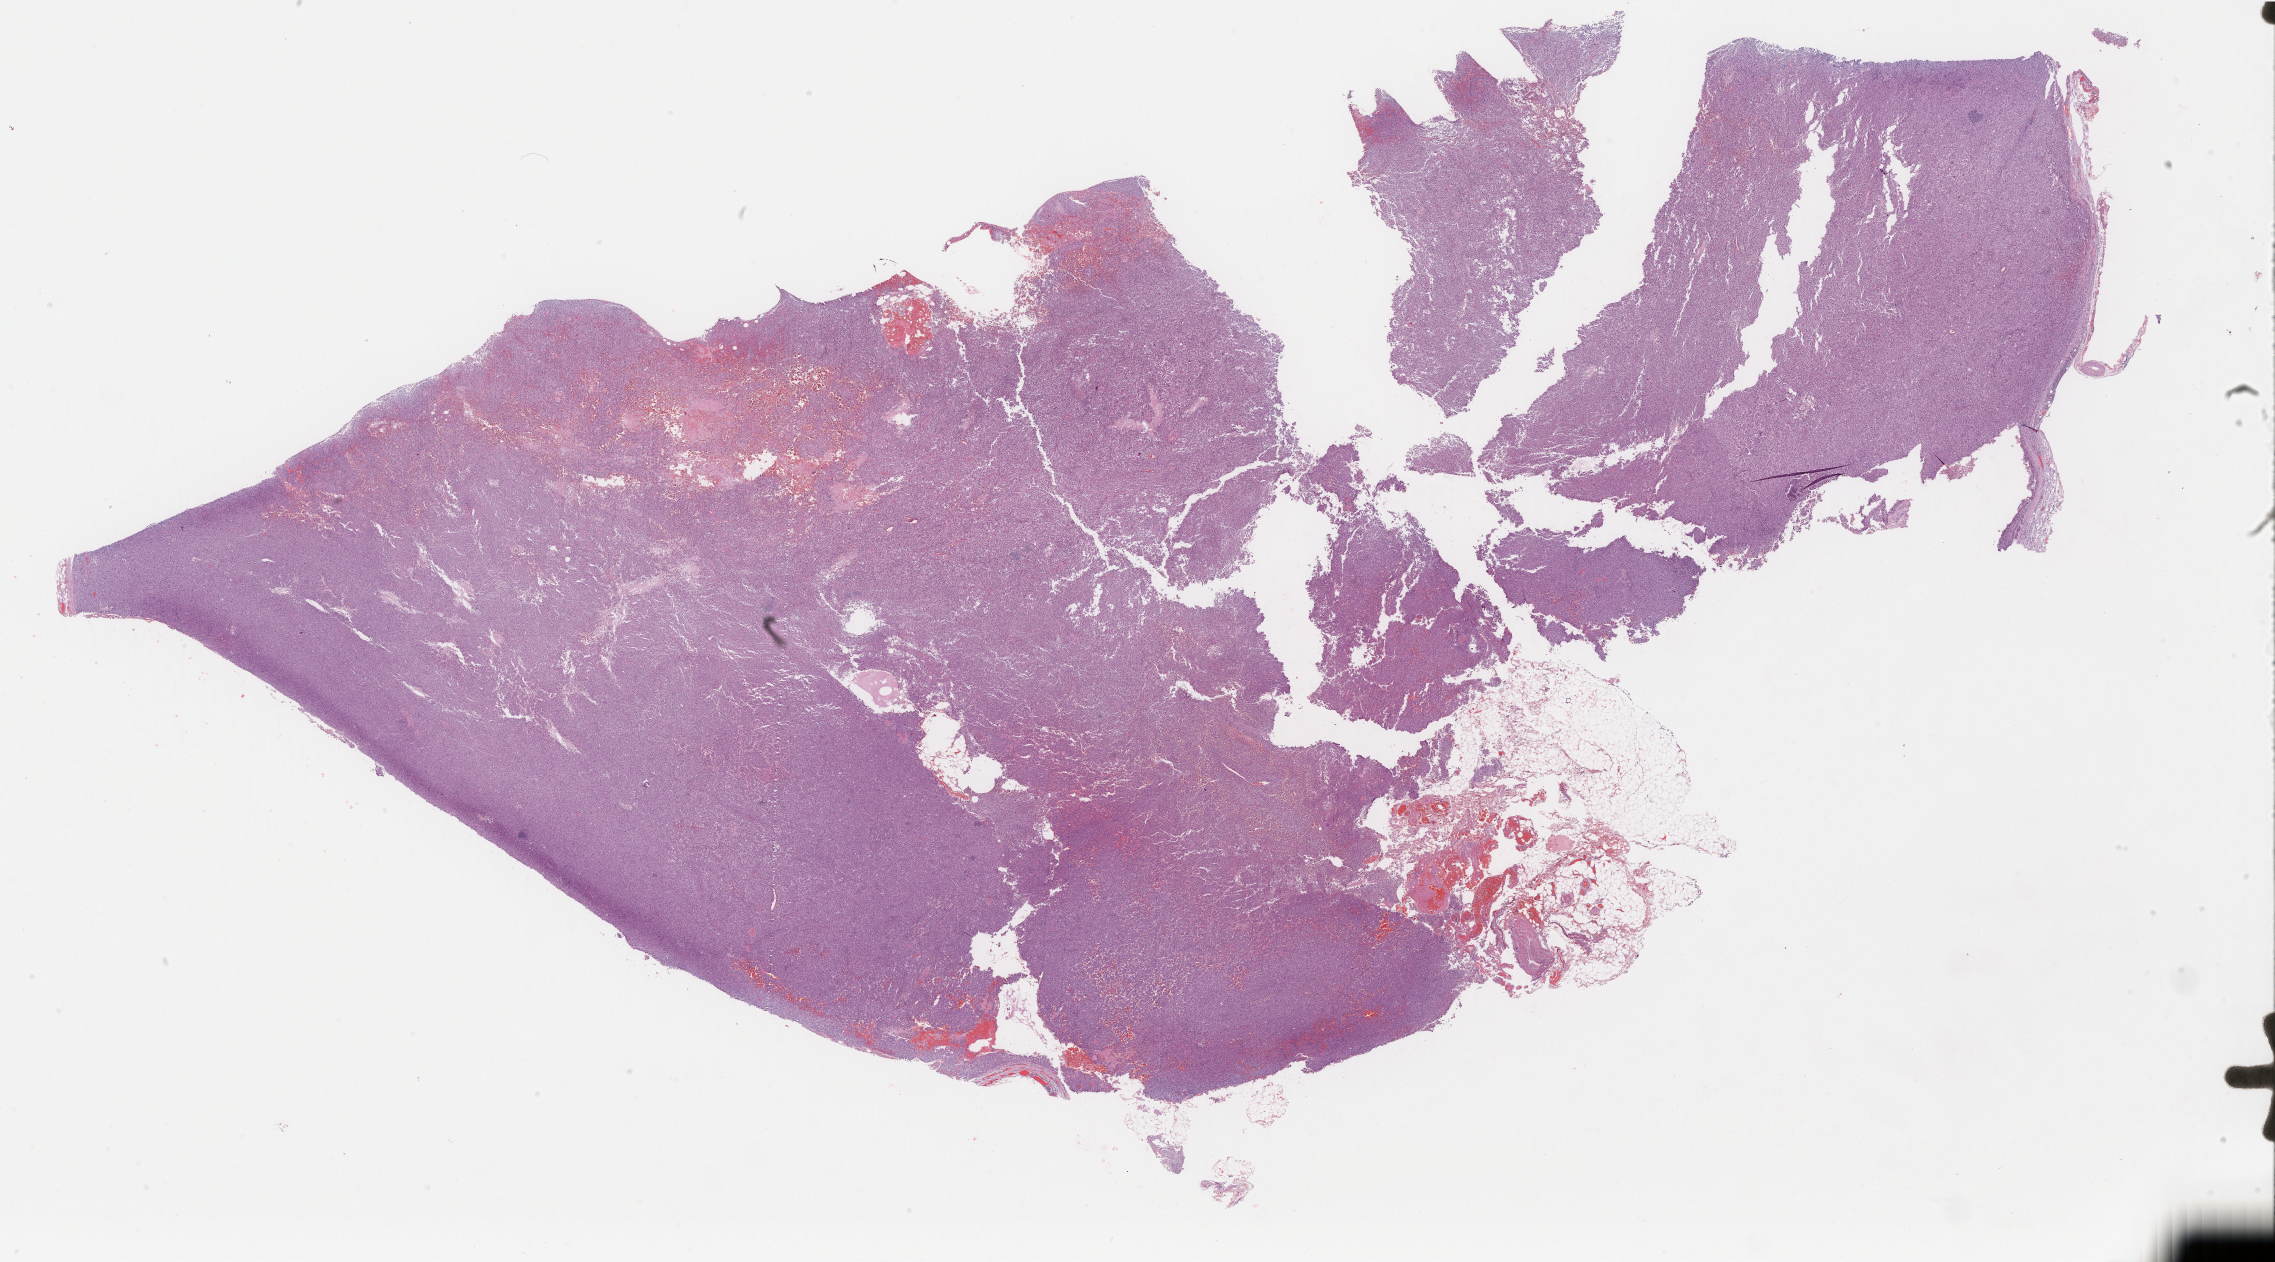
H&E-stained whole-slide image — a low-resolution overview of the entire scanned area, about 36.1 x 20.0 mm (from a 40x scan). Formalin-fixed paraffin-embedded (FFPE) diagnostic section. Primary tumour sample from the skin. Female, age 72 years at initial diagnosis.
Histologic diagnosis: Malignant melanoma, NOS.